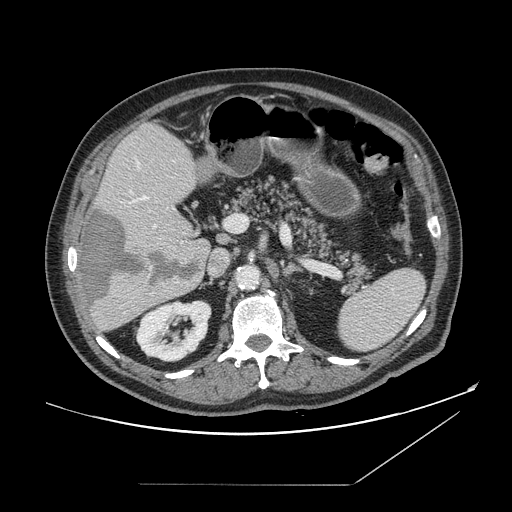
Contrast-enhanced abdominal CT, one axial slice. Position 86 of 166 along the scan axis. 120 kVp. Intravenous contrast given. Soft-tissue window (W 400 / L 40 HU). 2.5 mm slice thickness. 512 × 512 image matrix, field of view 416 × 416 mm. Male patient, age 80 years. Case-level facts recorded for this patient, not image findings: diagnosis: colorectal cancer liver metastases, imaged before liver resection; multiple liver metastases: no; largest metastasis: 2.2 cm; disease in both lobes: no.
Outlined on this slice (expert manual segmentation):
- hepatic veins: bounding box [x1, y1, x2, y2] px = [135, 161, 148, 202]
- liver: [78, 124, 210, 332]
- planned liver remnant (the part of the liver to remain after resection): [100, 124, 198, 237]
- portal vein (with intrahepatic branches): [130, 192, 231, 243]
- liver metastasis: [80, 209, 202, 312]